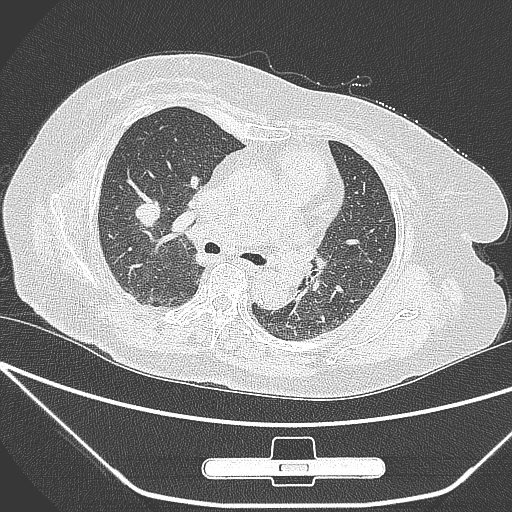
Chest CT, one axial slice; position 160 of 245 along the scan axis; 120 kVp; lung window (W 1500 / L -600 HU); 1 mm slice thickness; 512 × 512 image matrix. Female patient, age 65 years. Case-level facts recorded for this patient, not image findings: clinical TNM (as recorded): T1c N0 M0.
Outlined on this slice (rectangle marked by the reading radiologist):
- lung tumour (recorded histology: adenocarcinoma): bounding box <130,195,166,233> (left, top, right, bottom; pixels)